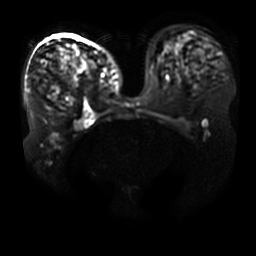
Breast MRI, one axial slice; slice 23 of 41 in the series (ordered by position); diffusion-weighted series; image 2 of 4 stored at this slice position (different b-values; order by instance number); 3 T; 5 mm slice thickness; 256 × 256 image matrix, field of view 400 × 400 mm. Female patient.
Structures marked on this image (expert manual segmentation):
- tumour on diffusion-weighted imaging: bounding box (x1, y1, x2, y2) in pixels: (64, 46, 95, 67)